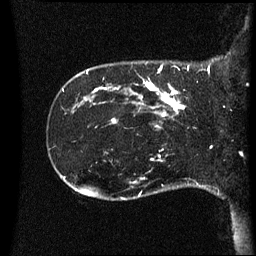
Breast MRI (dynamic contrast-enhanced), one sagittal slice; slice 10 of 60 in the series (ordered by position); dynamic contrast-enhanced series, image 2 of 3 at this slice position (ordered by acquisition); 1.5 T; TE 4.2 ms, TR 8.4 ms; 2.2 mm slice thickness; 256 × 256 image matrix, field of view 220 × 220 mm. Female patient, age 41 years. Case-level facts recorded for this patient, not image findings: setting: breast cancer imaged before/during neoadjuvant chemotherapy; receptor status: HER2-positive.
Outlined on this slice (semi-automatically segmented with operator editing):
- analysis volume of interest (the breast-tissue region the enhancement analysis was run in; not a lesion): bounding box (x1, y1, x2, y2) in pixels: (123, 80, 189, 125)
- tumour enhancement mask (voxels above the 70 % enhancement threshold inside the analysis volume of interest): (137, 80, 186, 117)